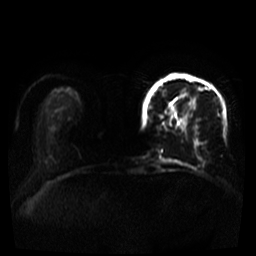
Breast MRI, one axial slice. Slice 9 of 39 in the series (ordered by position). Diffusion-weighted series; image 2 of 4 stored at this slice position (different b-values; order by instance number). 3 T. 5 mm slice thickness. 256 × 256 image matrix, field of view 320 × 320 mm. Female patient.
Structures marked on this image (outlined manually by an expert reader):
- tumour on diffusion-weighted imaging: bounding box (x1, y1, x2, y2) in pixels: (180, 90, 196, 105)